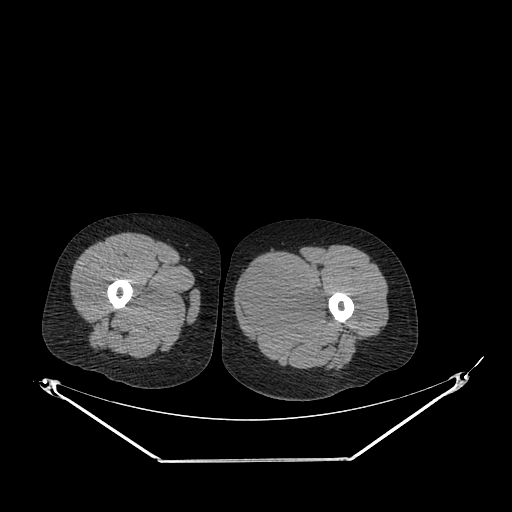
CT of an extremity soft-tissue mass (from a PET/CT study), one axial slice; position 233 of 267 along the scan axis; 120 kVp; soft-tissue window (W 400 / L 40 HU); 3.75 mm slice thickness; 512 × 512 image matrix. Female patient. Case-level facts recorded for this patient, not image findings: histological type: pleiomorphic leiomyosarcoma; grade: intermediate; site of the primary tumour: left thigh.
Structures marked on this image (expert contour drawn on MRI and transferred to this co-registered scan by the dataset authors):
- gross tumour volume including surrounding oedema: bounding box (x1, y1, x2, y2) in pixels: (237, 263, 332, 336)
- gross tumour volume (mass): (237, 263, 327, 334)